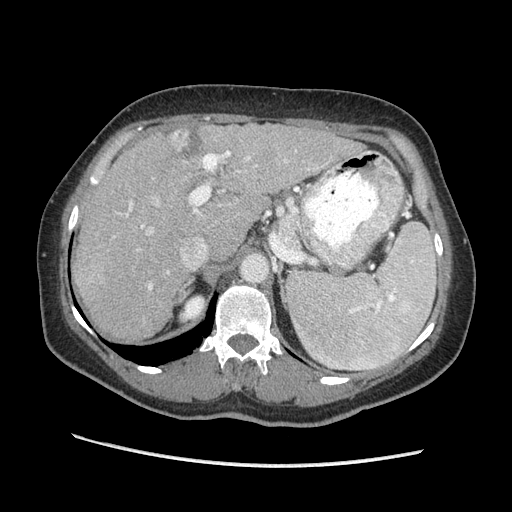
Contrast-enhanced abdominal CT (liver protocol), one axial slice. Slice 137 of 170 in the series (ordered by position). Reconstruction kernel STANDARD. Soft-tissue window (W 400 / L 40 HU). 2.5 mm slice thickness. 512 × 512 image matrix, field of view 360 × 360 mm. Case-level facts recorded for this patient, not image findings: diagnosis: hepatocellular carcinoma (patient treated with transarterial chemoembolisation; whether this scan precedes or follows treatment is not stated here); TNM stage (as recorded): Stage-II; Child-Pugh class: A; tumour nodularity: multinodular; tumour size: 4 cm.
Structures marked on this image (semi-automatically segmented with operator editing):
- liver parenchyma outside the tumour (the mass and vessels are separate outlines, so this box may not span the whole liver): bounding box (x1, y1, x2, y2) in pixels: (72, 122, 364, 340)
- mass: (164, 128, 205, 161)
- liver vessels: (126, 151, 328, 290)